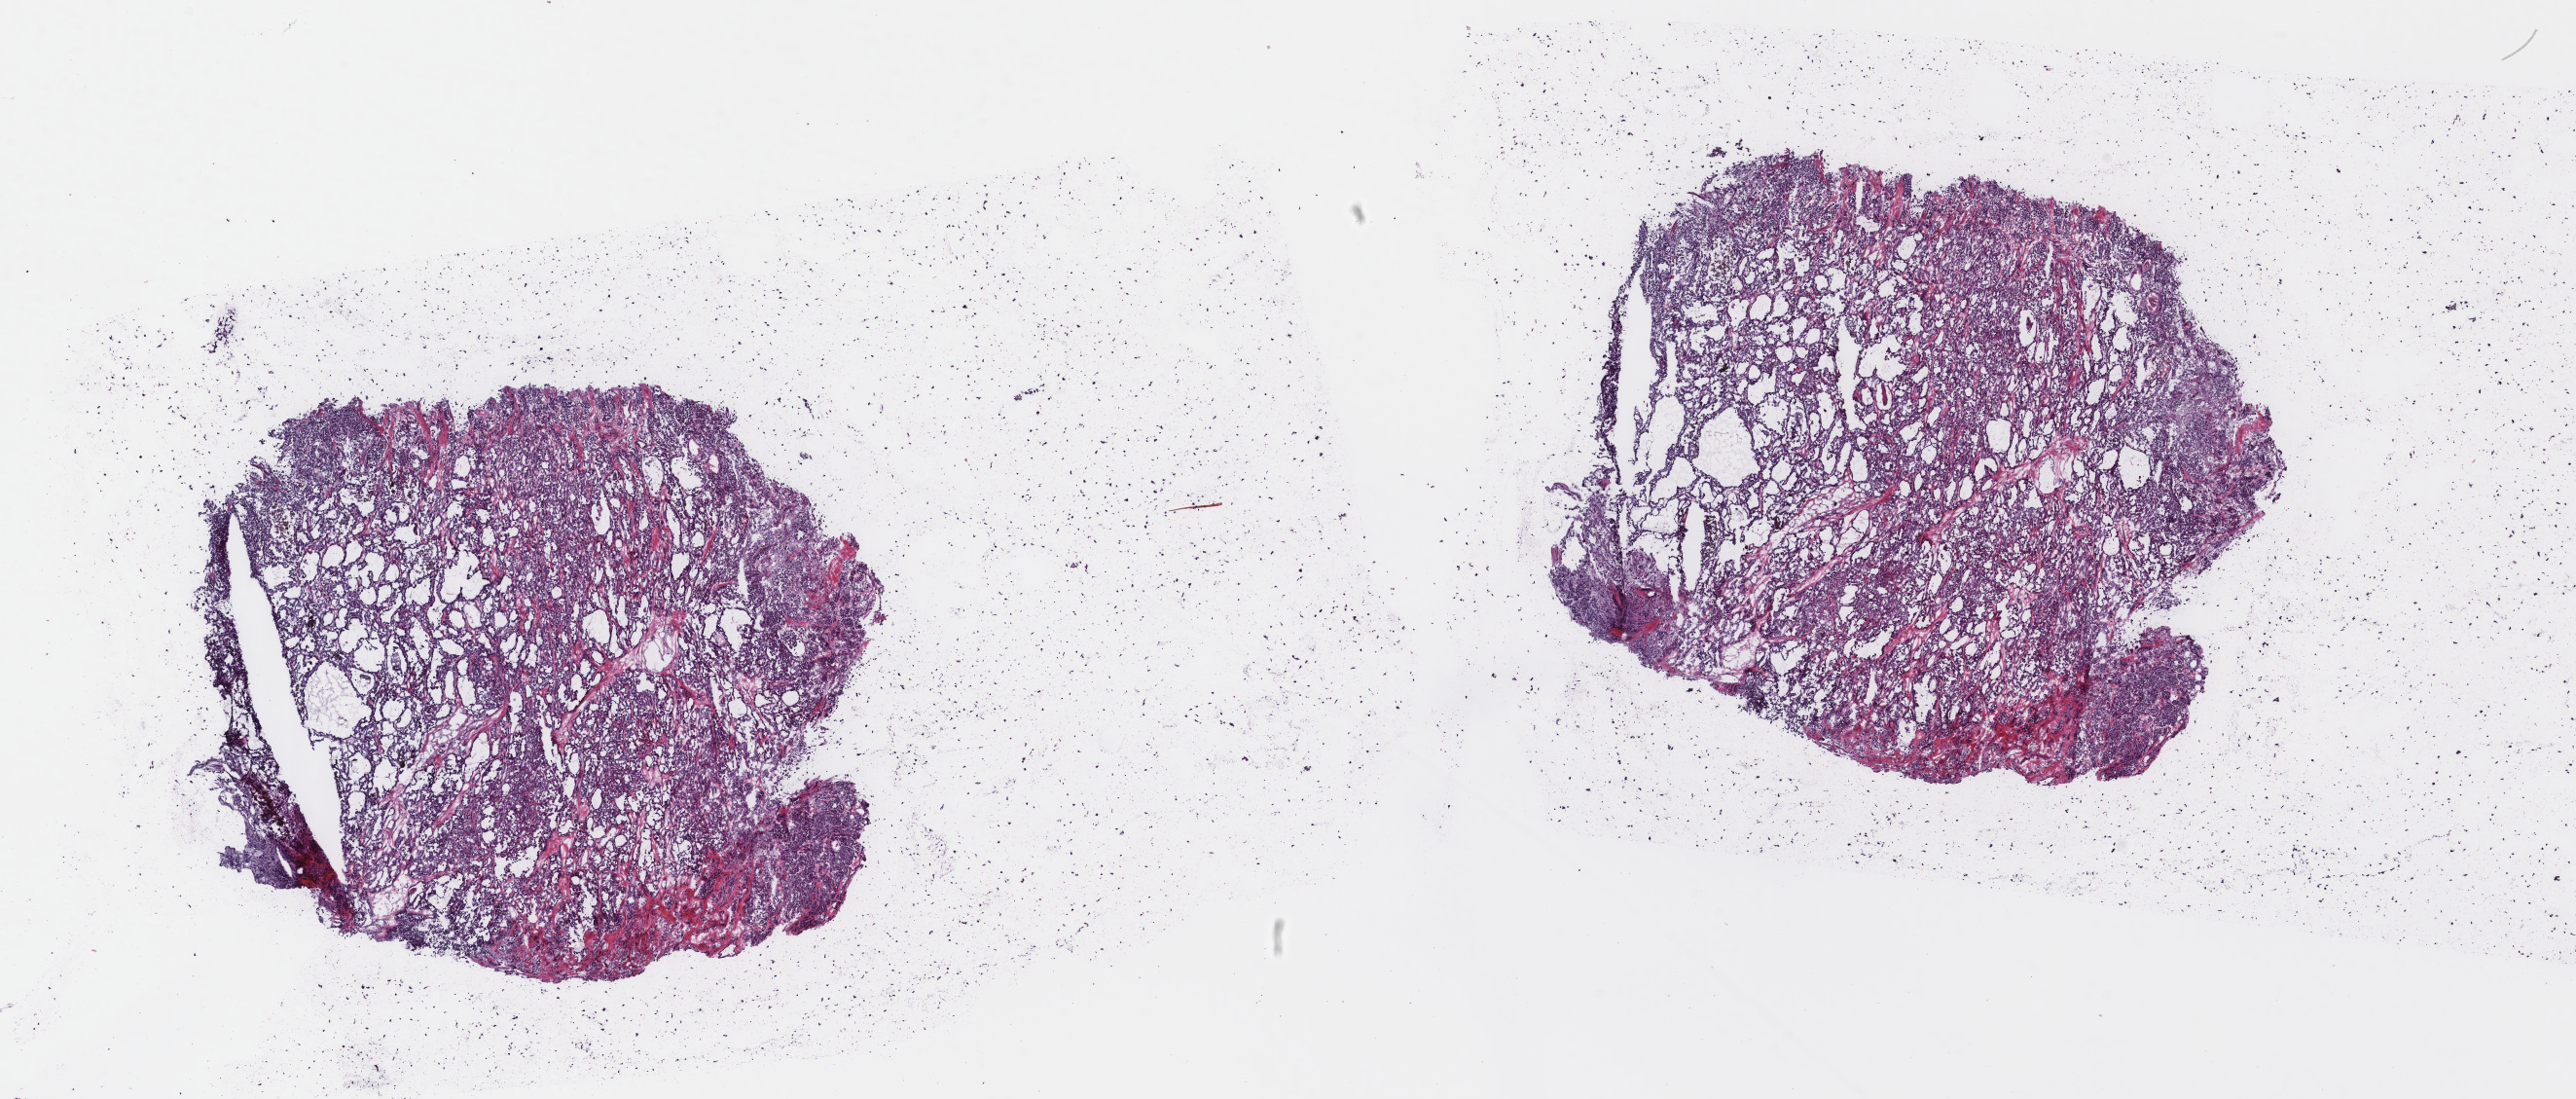
Digitized H&E-stained tissue section (whole slide), shown as a low-resolution overview of the whole scanned area (about 21.0 x 9.0 mm), frozen section from the top of the tissue portion, thyroid, primary tumour sample. Patient: female, age at initial diagnosis 54 years. Composition of this section per pathologist review: tumour cells 100%, tumour nuclei 90%, normal cells 0%, stromal cells 0%, necrosis 0%. Inflammatory infiltration, as recorded: lymphocyte infiltration 0%, monocyte infiltration 0%, neutrophil infiltration 0%.
- histologic diagnosis: Oxyphilic adenocarcinoma
- AJCC pathologic stage: III (7th edition)
- laterality: left